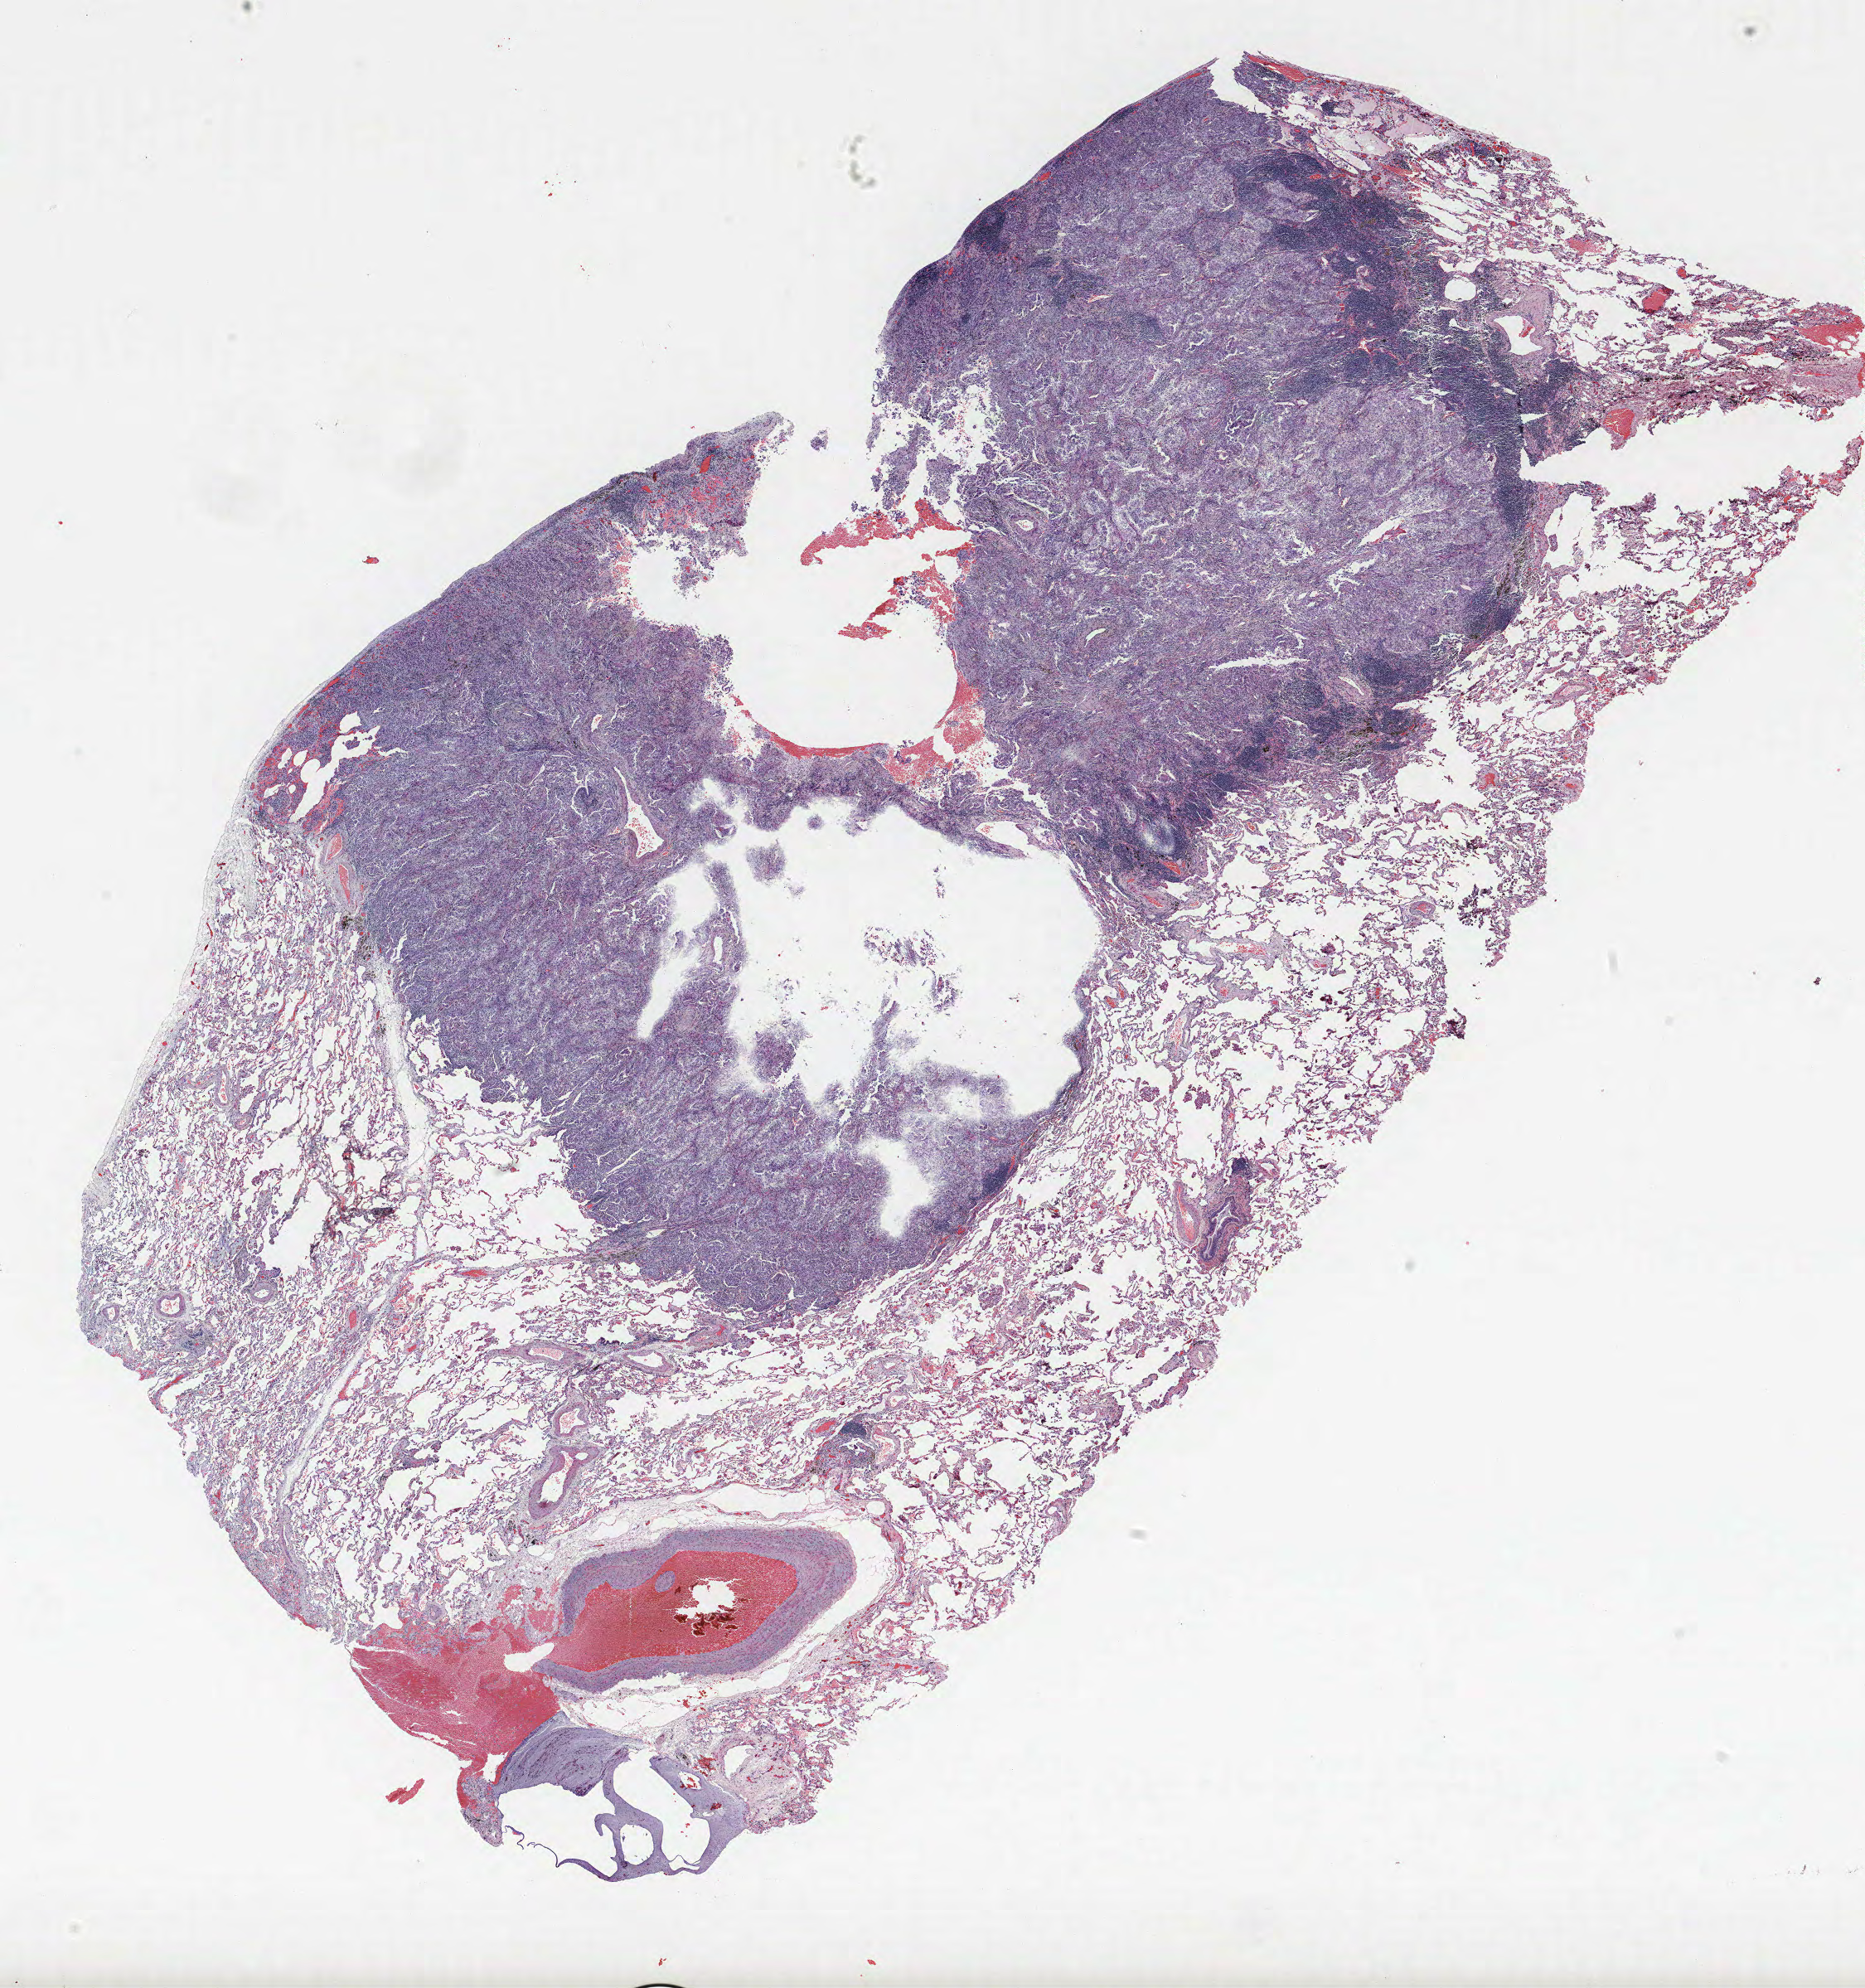
H&E-stained whole-slide image — low-resolution overview of the scanned area, about 18.0 x 19.2 mm (from a 40x scan); FFPE section; lung. Female patient, aged 62 at enrolment. Current smoker at enrolment.
Participant's lung-cancer diagnosis: Adenocarcinoma, NOS (ICD-O-3 8140/3).